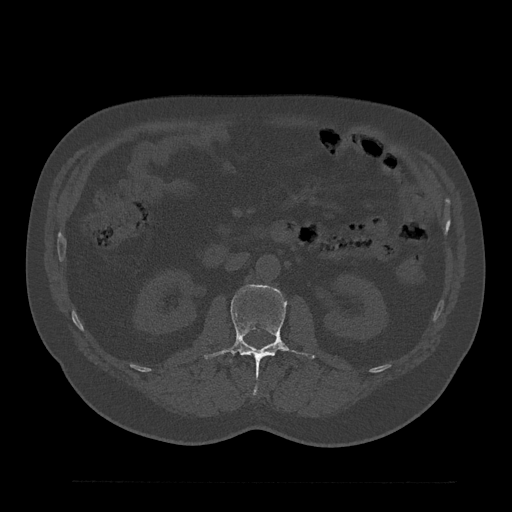
CT including the spine, one axial slice; reconstruction kernel Br40s/3; 120 kVp; bone window (W 1800 / L 400 HU); 0.5 mm slice thickness; 512 × 512 image matrix, field of view 430 × 430 mm. Male patient, age 61 years. Case-level facts recorded for this patient, not image findings: primary cancer: prostate.
Annotated regions visible in this slice (semi-automatic segmentation, software-assisted and operator-edited):
- L2 vertebra: bounding box (x1, y1, x2, y2) in pixels: (204, 285, 316, 374)